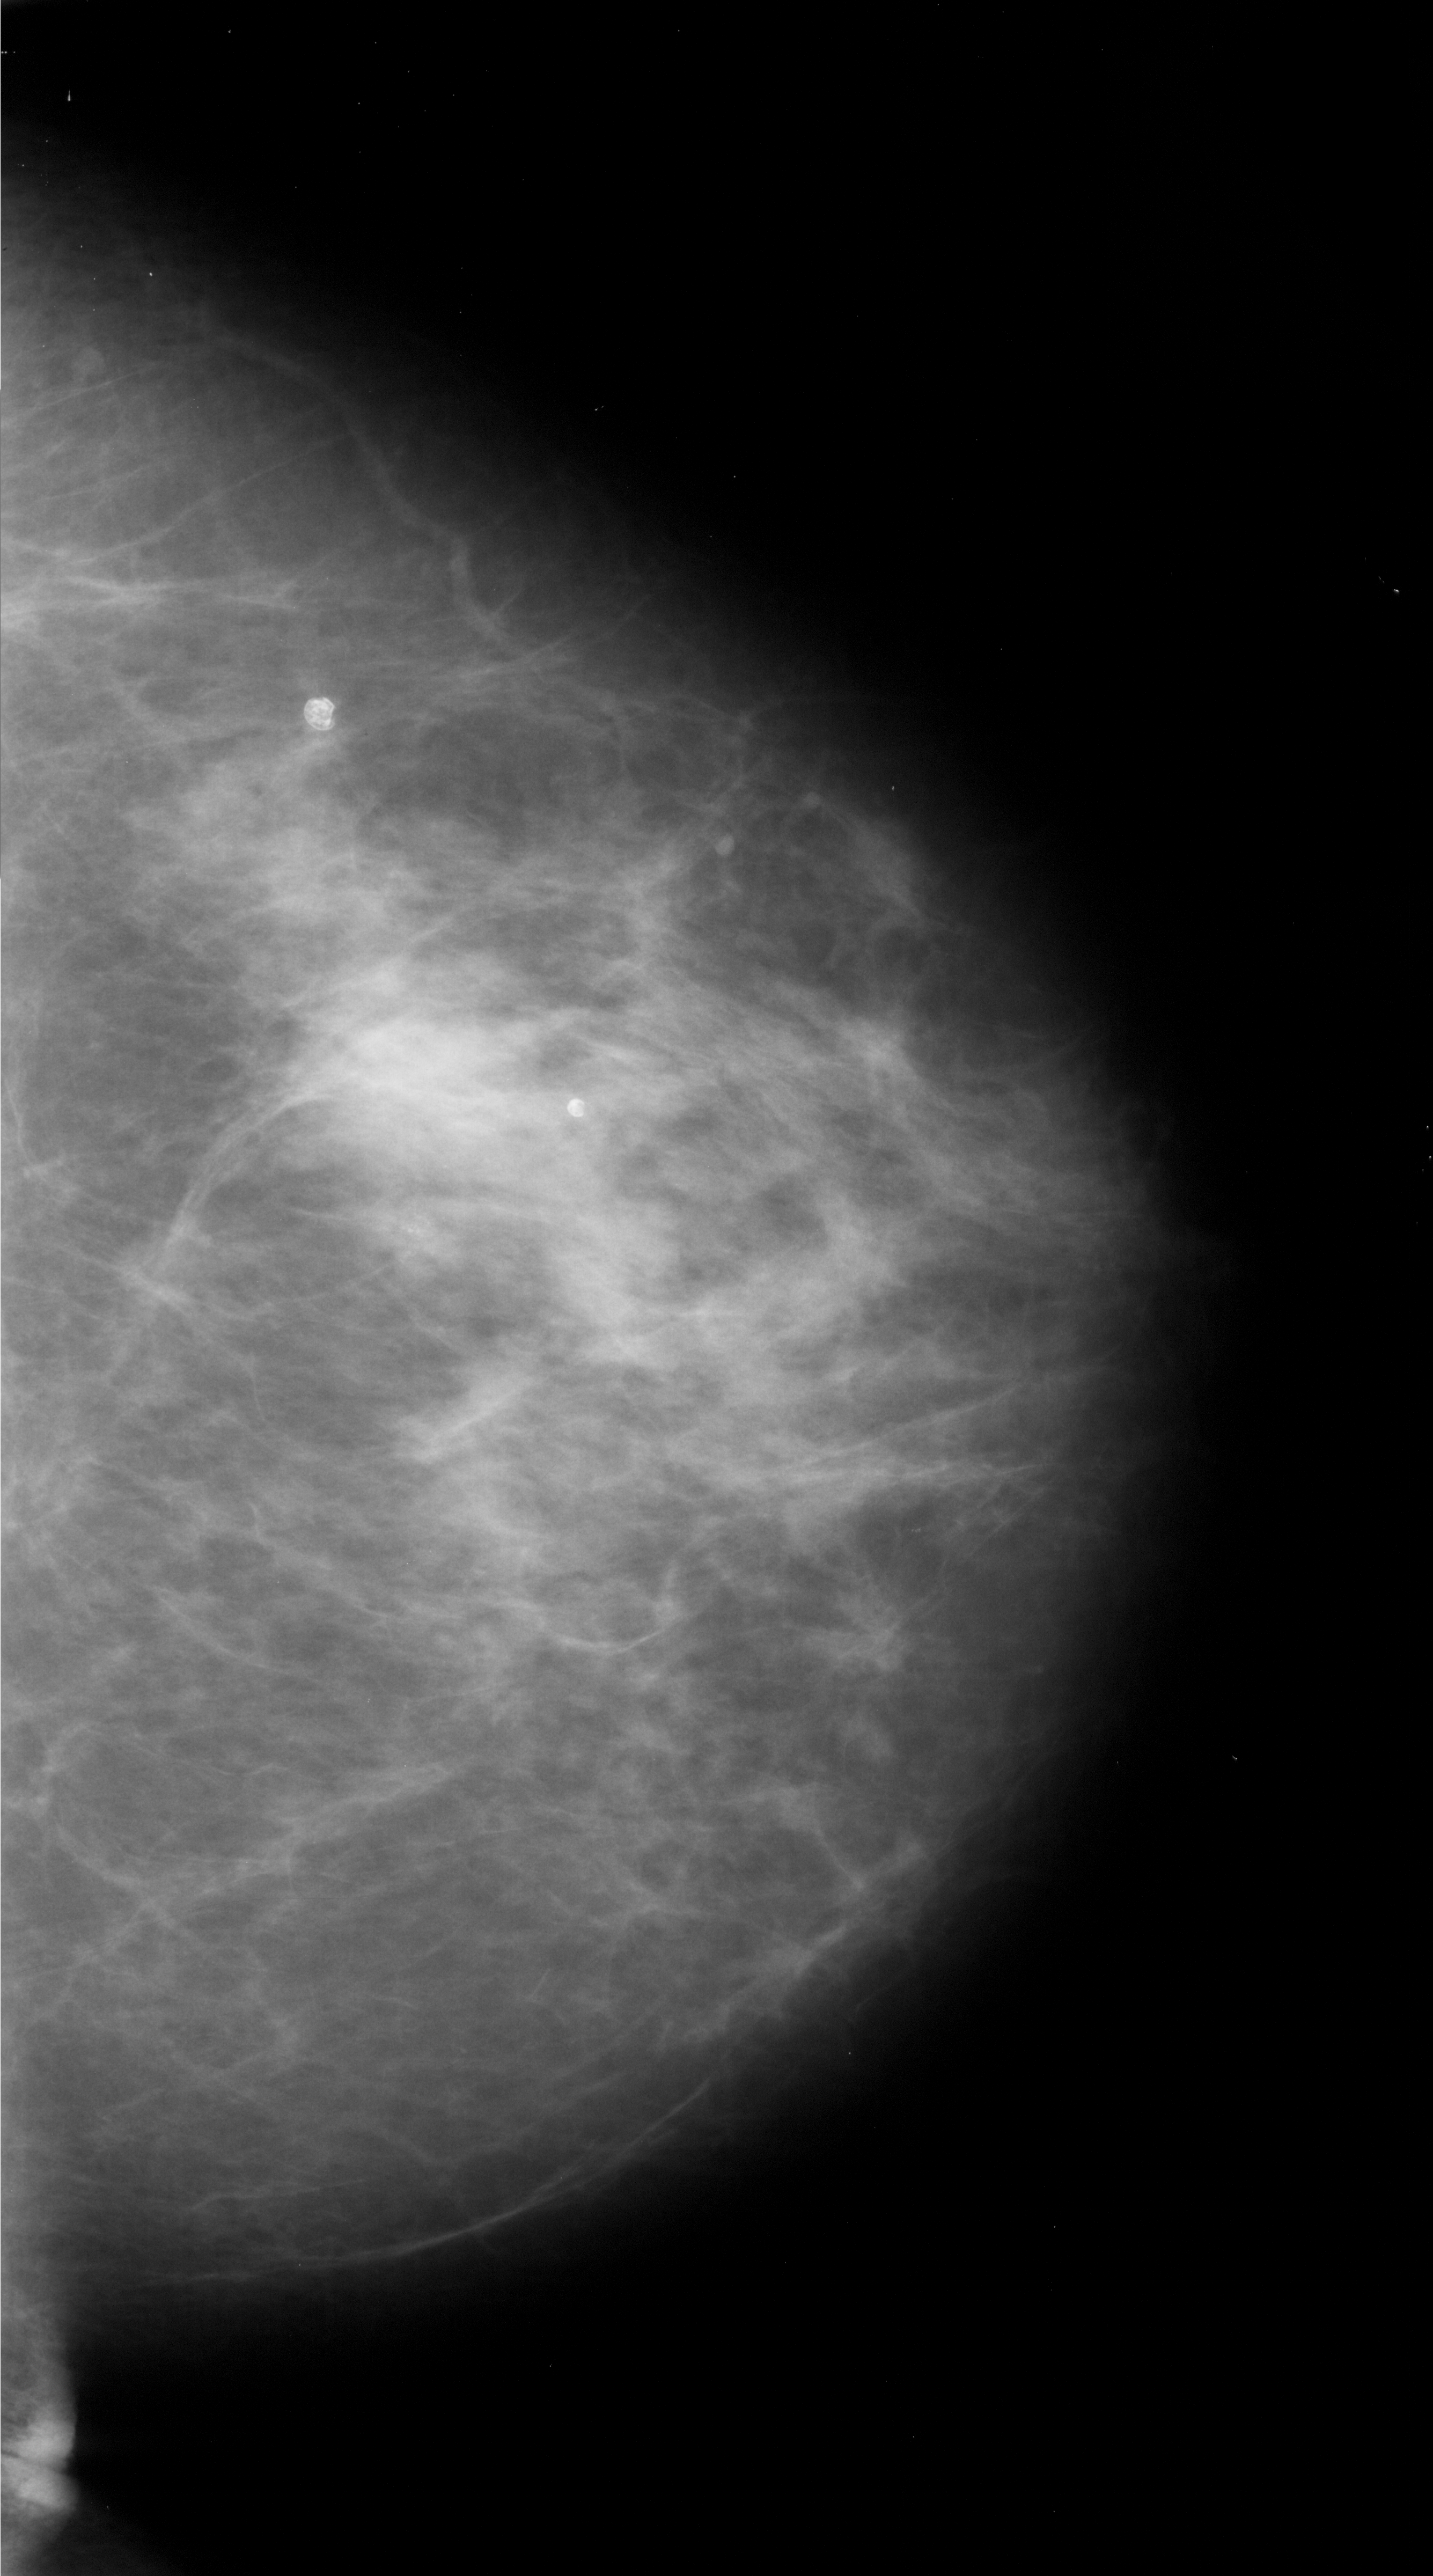
Scanned film-screen mammogram. Right breast. Craniocaudal (CC) view. BI-RADS breast density category 3 (scale 1–4). 1433 × 2576 image matrix.
Expert-marked regions of interest on this image (one box per marked abnormality):
- calcifications, morphology pleomorphic, distribution linear; BI-RADS assessment category 4; subtlety rating 1 on a 1 (subtle) to 5 (obvious) scale; pathology (as recorded): malignant: bounding box (x1, y1, x2, y2) in pixels: (339, 1135, 536, 1290)